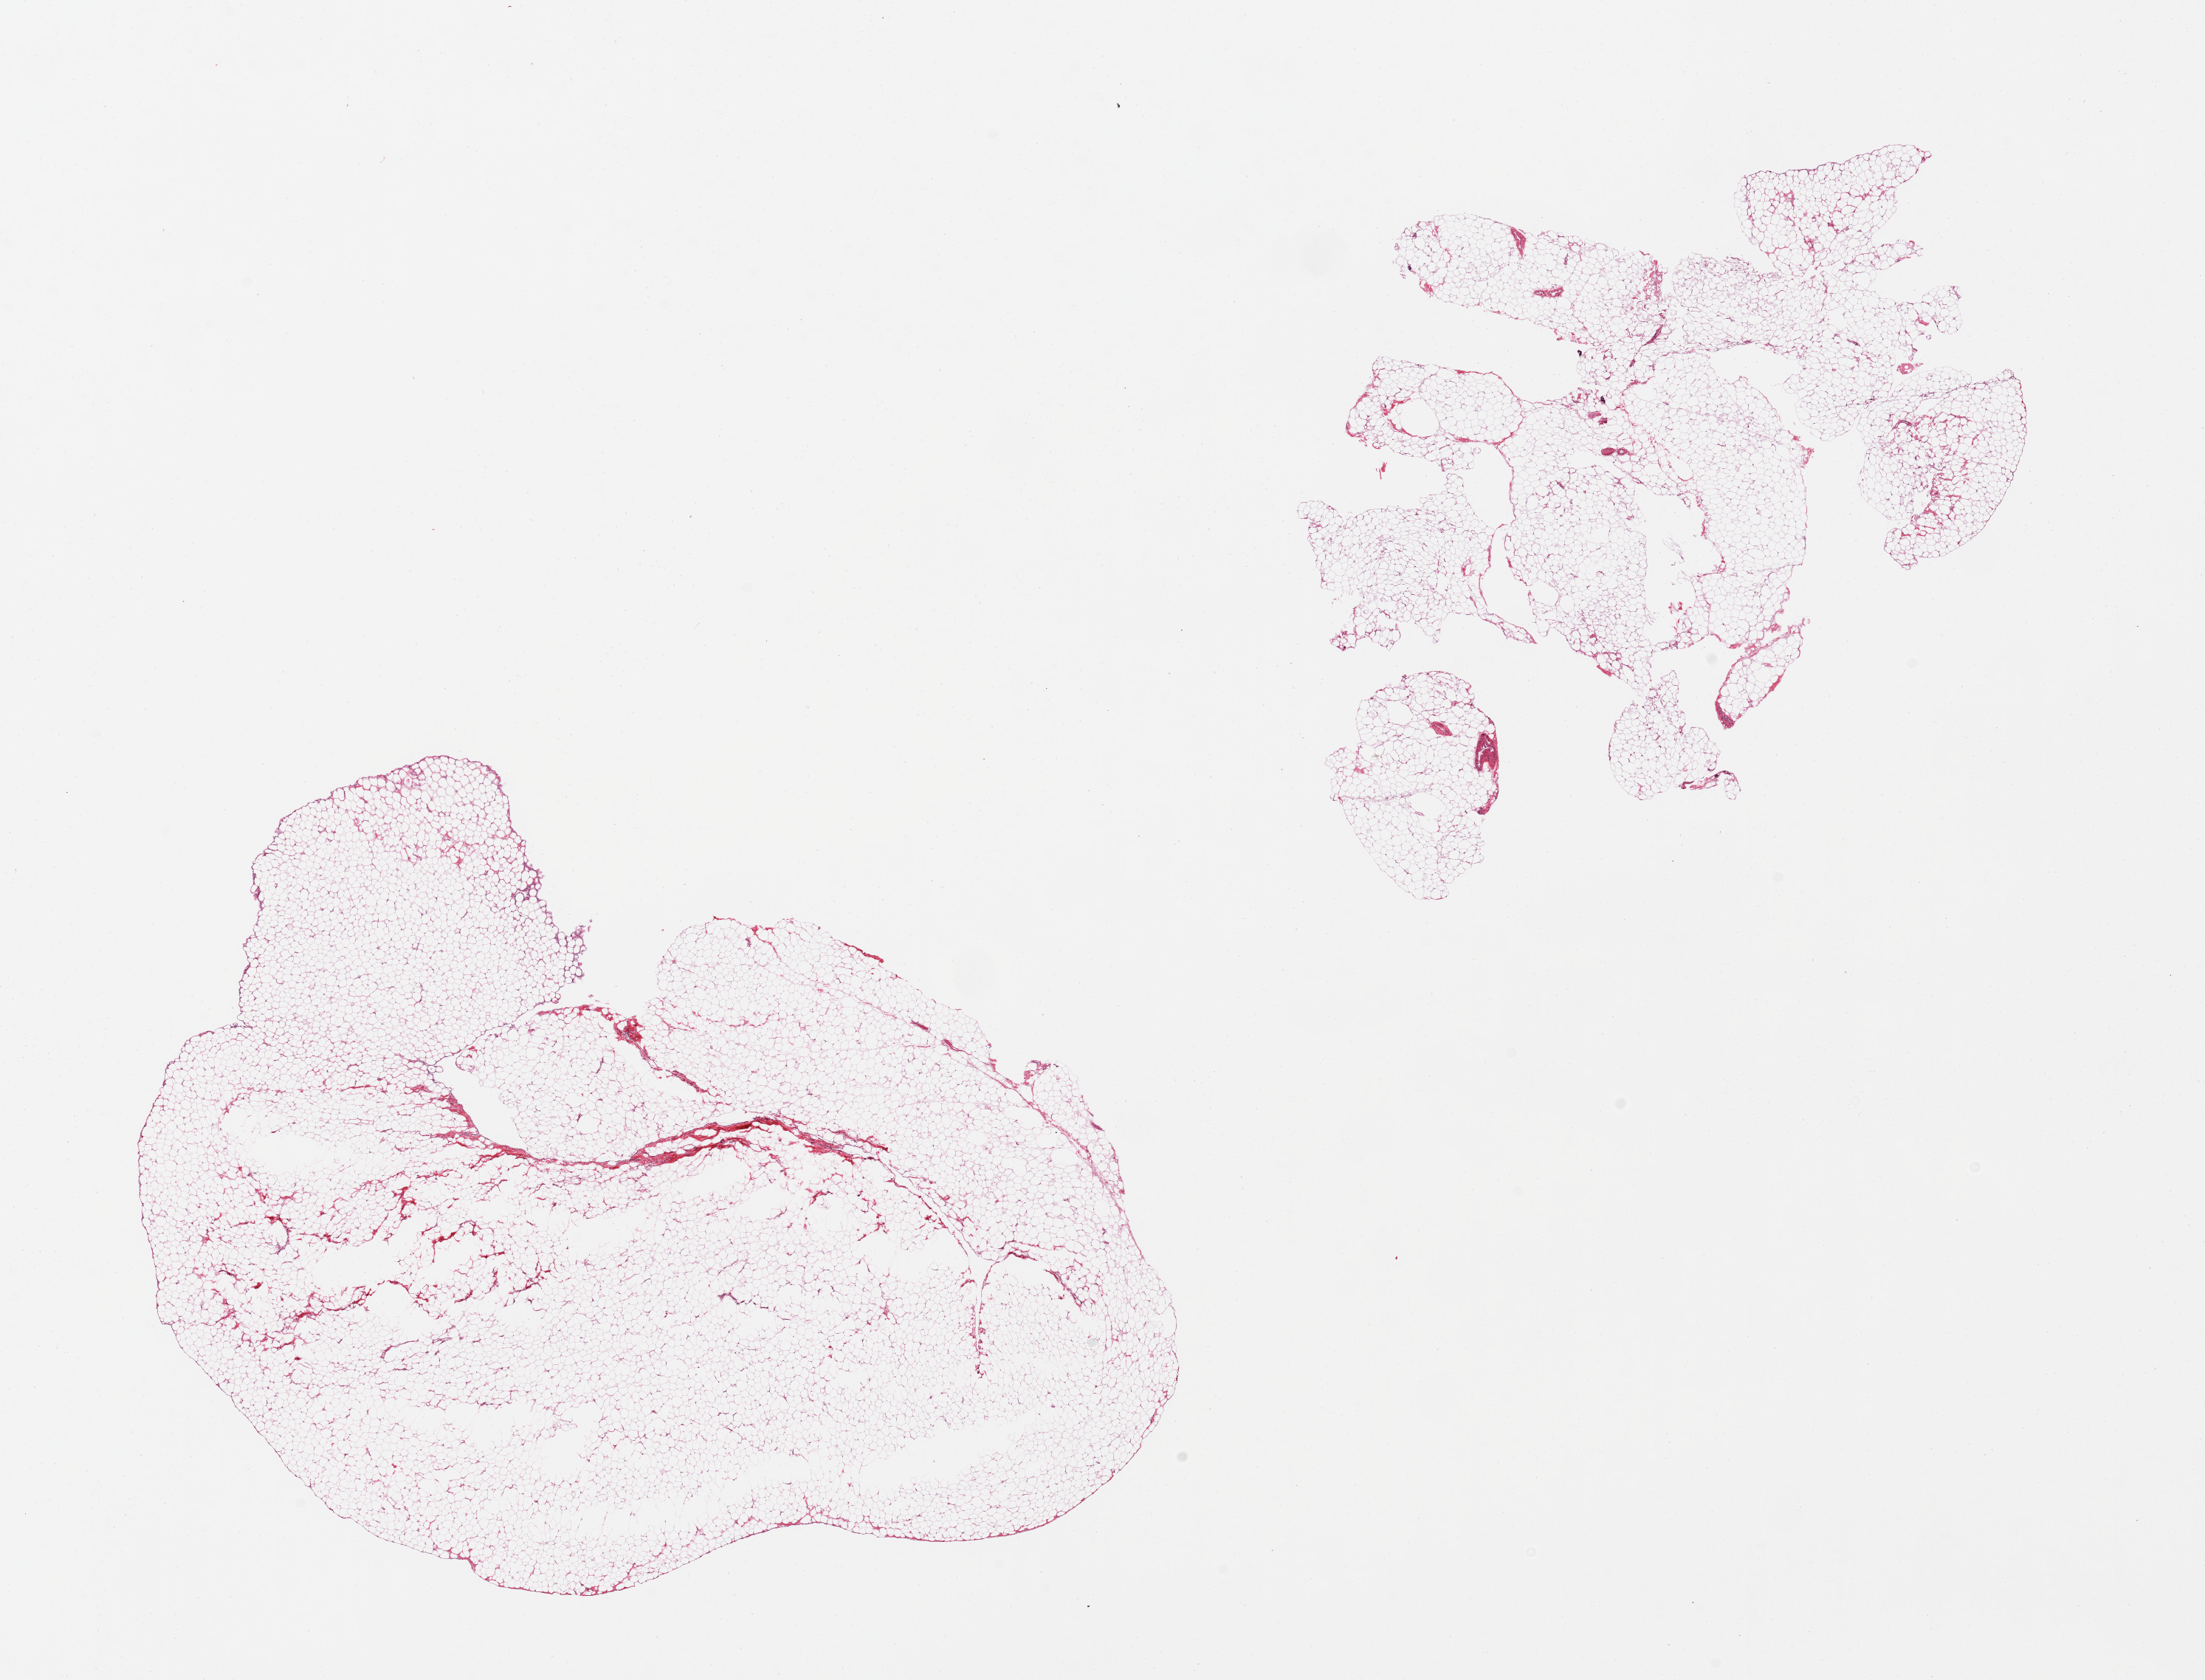
Digitized H&E-stained section, low-resolution overview of the scanned area, about 23.6 x 18.0 mm (from a 20x scan). PAXgene-fixed, paraffin-embedded tissue. Target tissue: omentum. Donor tissue sample. Female donor.
Pathologist's review note for this sample: 2 pieces.